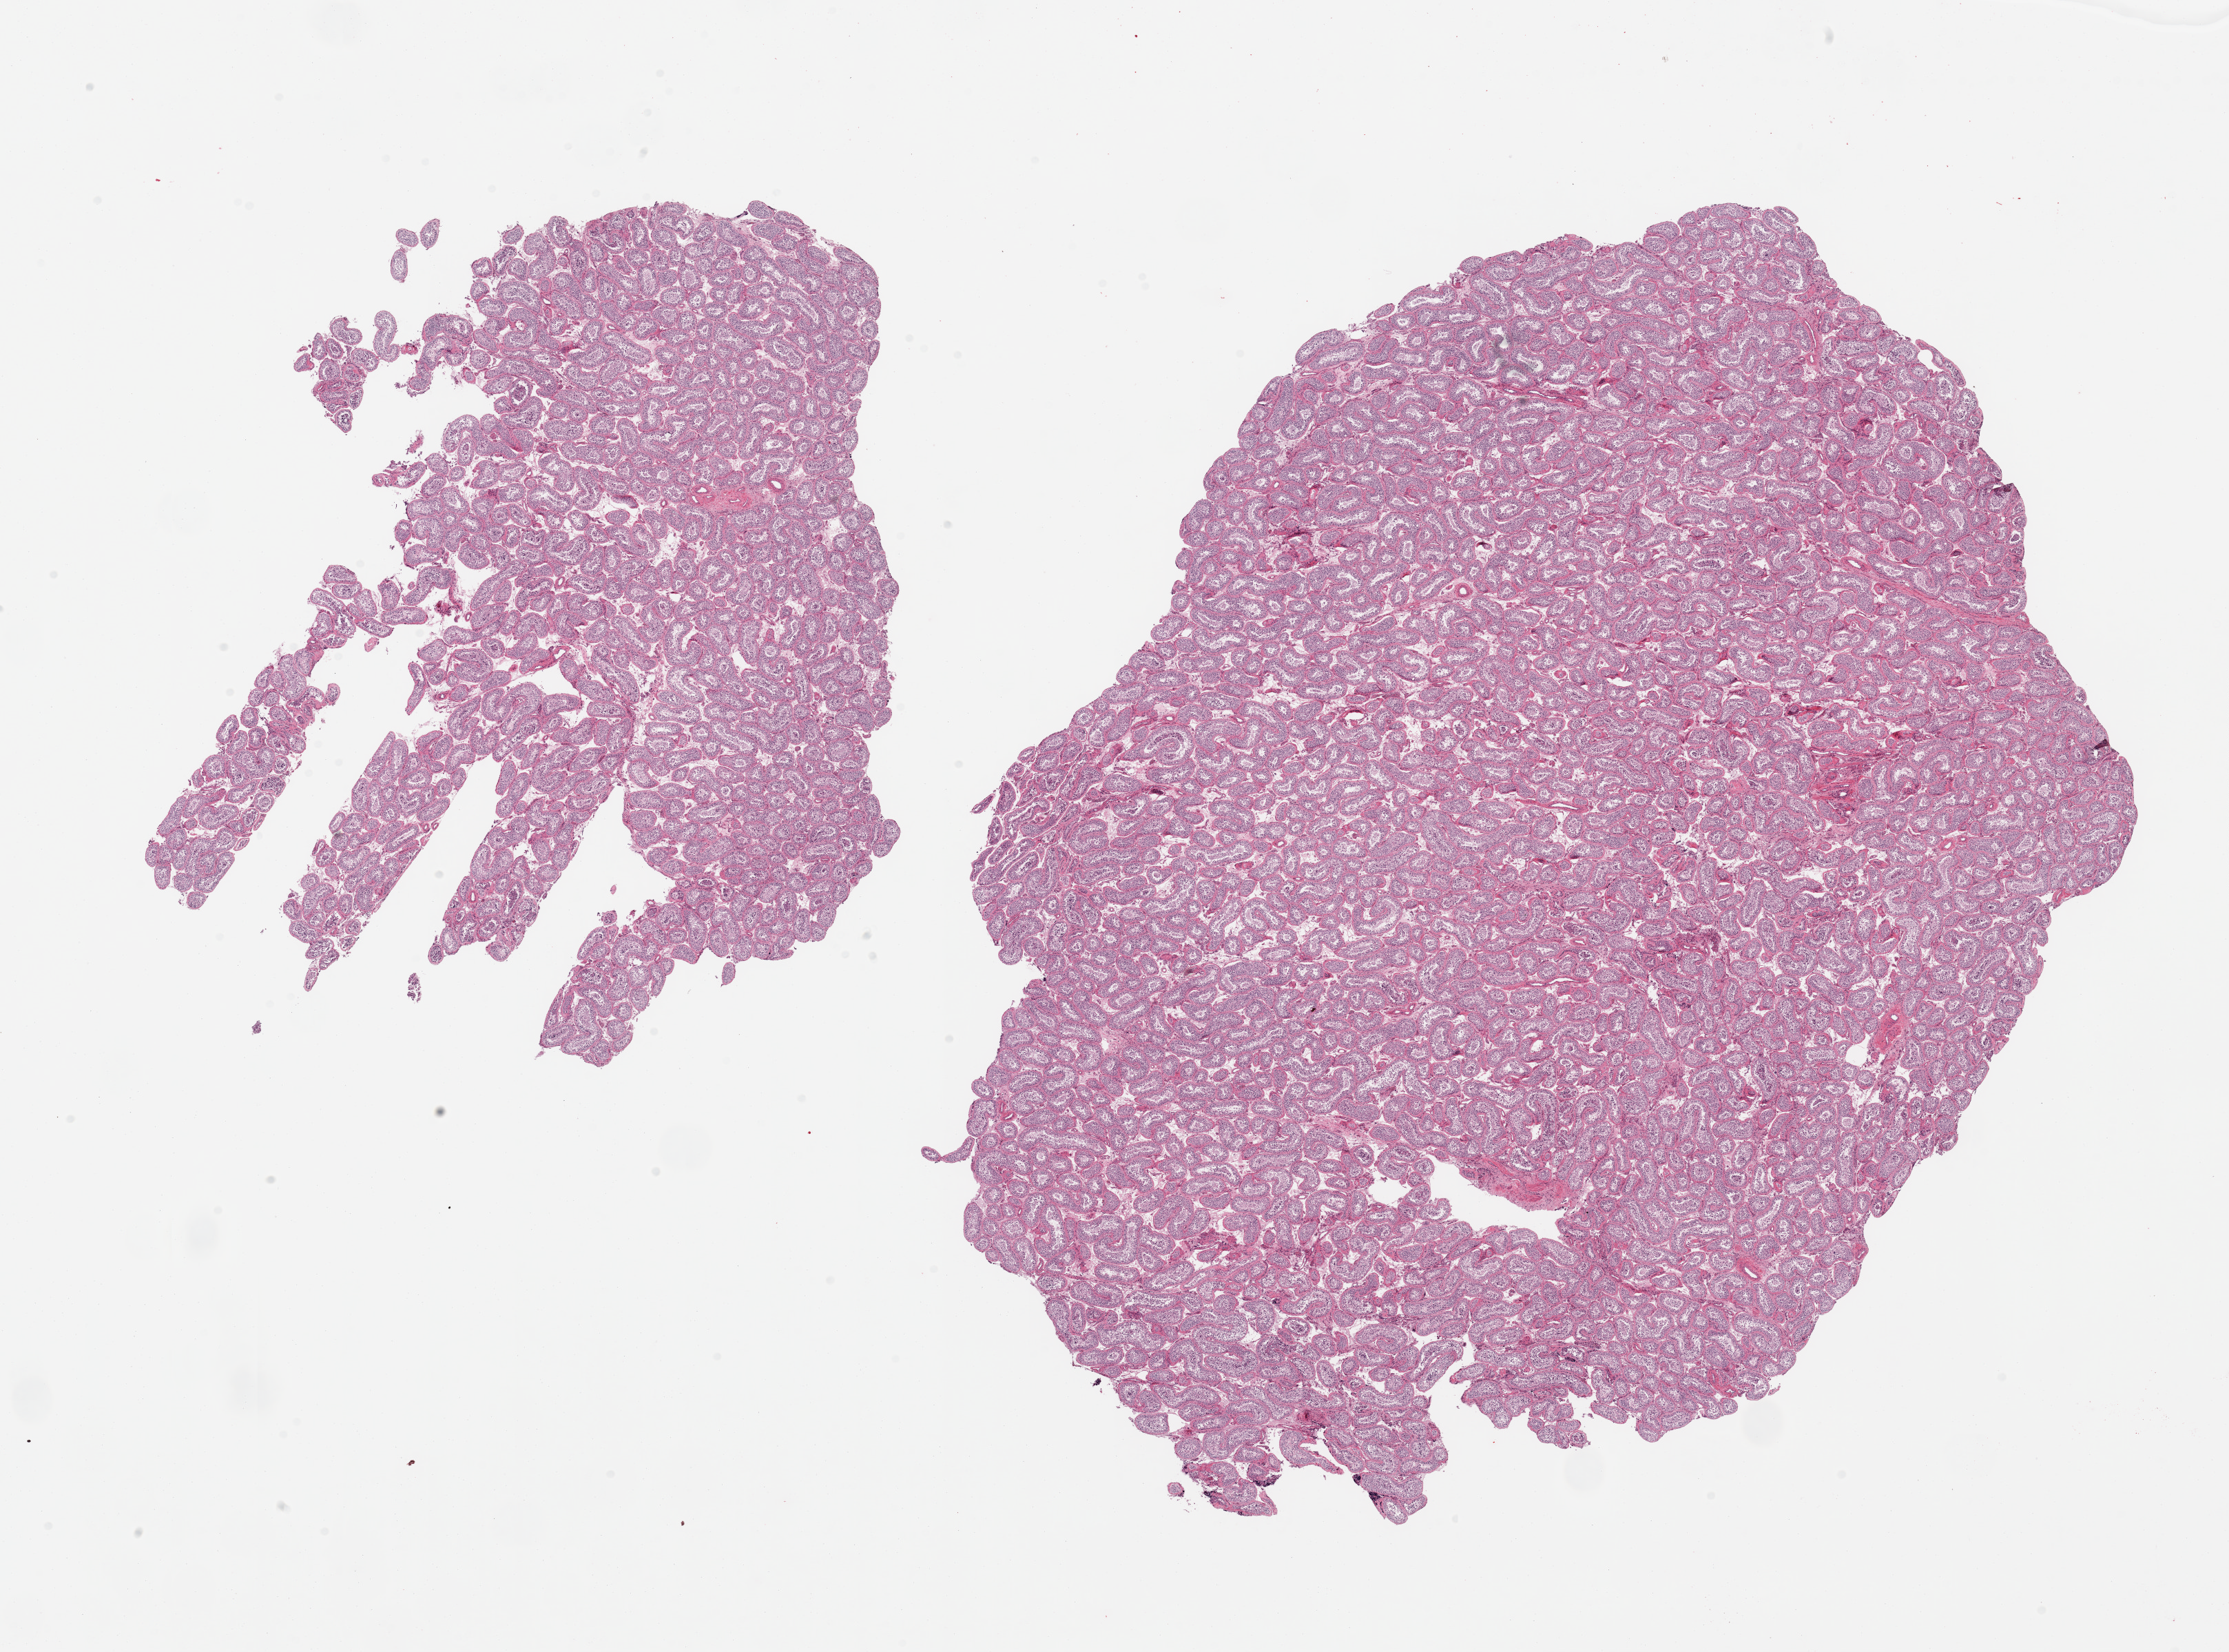
Digitized hematoxylin and eosin (H&E)-stained section, a low-resolution overview of the entire scanned area, about 25.6 x 19.0 mm (acquisition: 20x scan); PAXgene-fixed, paraffin-embedded tissue; section of testis (target tissue); donor tissue sample. Male donor.
• reviewer comment on this tissue sample: 2 pieces, well preserved; spermatogenesis is present